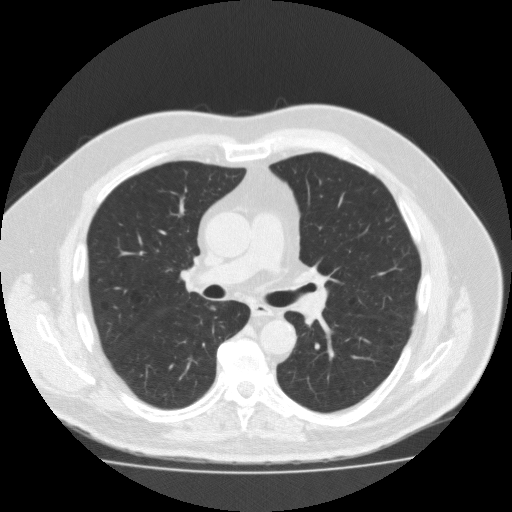
Low-dose screening chest CT, axial slice, second screening round (one year after baseline), lung window (W 1500 / L -600 HU), 120 kVp, slice 68 of 188 in the series, 512 × 512 image matrix, field of view 400 × 400 mm. Male participant, aged 56 years at enrolment. Current smoker at enrolment.
Expert-annotated lung lesion, bounding box (x1, y1, x2, y2) in pixels: (198, 298, 230, 320). Screening reader's record for this exam (one nodule recorded; not confirmed to be the boxed lesion): non-calcified nodule or mass ≥4 mm, right lower lobe, 5 × 5 mm, spiculated (stellate) margins, soft tissue attenuation, pre-existing on the prior screen: no. Official screen result: positive, change unspecified: nodule(s) >= 4 mm or enlarging nodule(s), mass(es), or other non-specific abnormalities suspicious for lung cancer. Lung cancer was diagnosed 448 days after this screen (after the third annual screen): adenocarcinoma, NOS, right lower lobe, moderately differentiated (G2), stage IA (AJCC 6th edition), 12 mm at pathology.